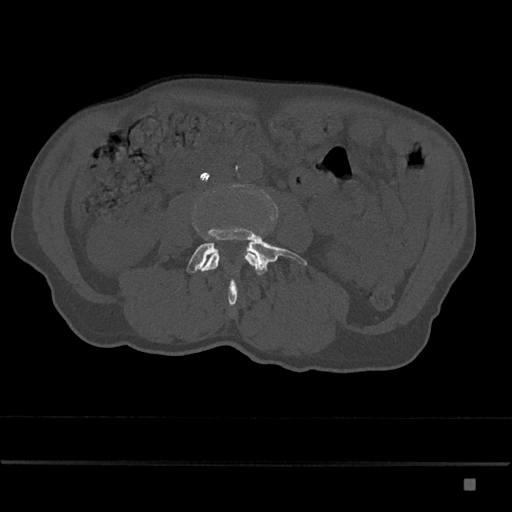
CT including the spine, one axial slice; position 365 of 797 along the scan axis; reconstruction kernel Br40s/3; bone window (W 1800 / L 400 HU); 0.5 mm slice thickness; 512 × 512 image matrix, field of view 390 × 390 mm. Male patient, age 72 years. Case-level facts recorded for this patient, not image findings: primary cancer: prostate.
Annotated regions visible in this slice (semi-automatically segmented with operator editing):
- L3 vertebra: bounding box [x1, y1, x2, y2] px = [202, 253, 258, 271]
- L4 vertebra: [187, 227, 307, 305]